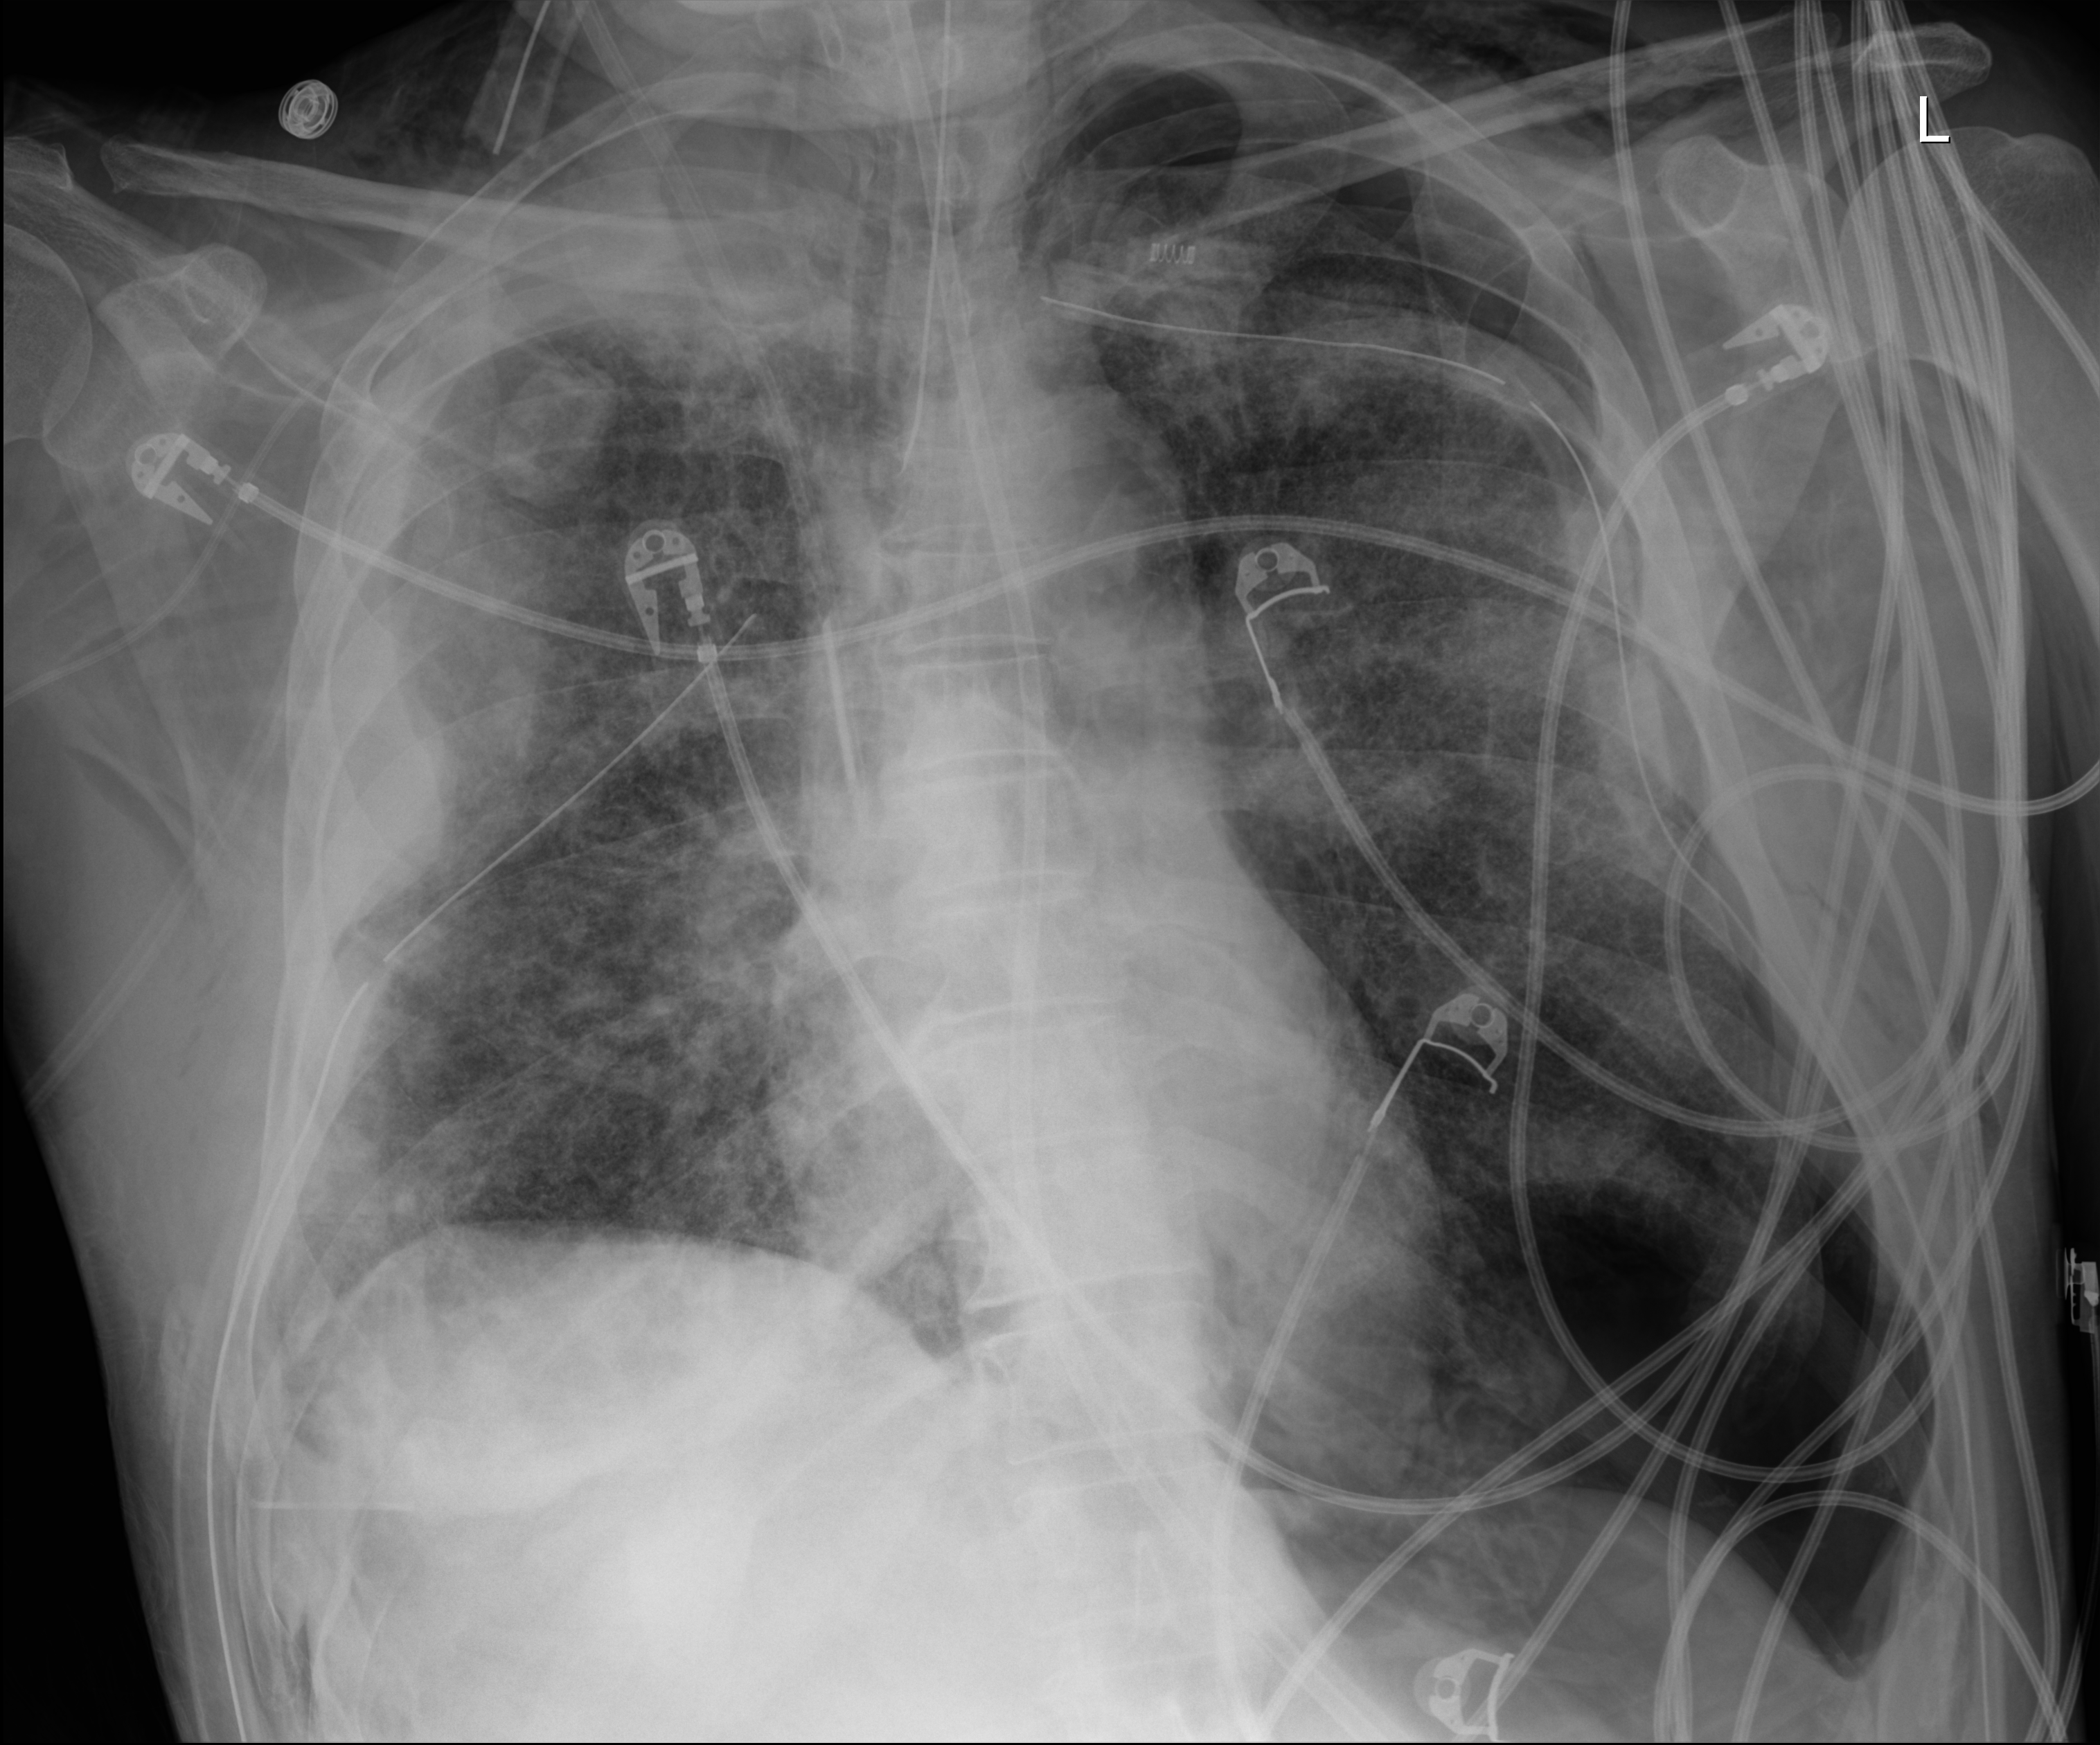
Chest radiograph, anteroposterior (AP) projection. Male patient hospitalised with COVID-19, age 18–59 years.
Admission-level facts for this patient (not findings on this image; timing relative to this image not recorded): length of hospital stay: 42 days.